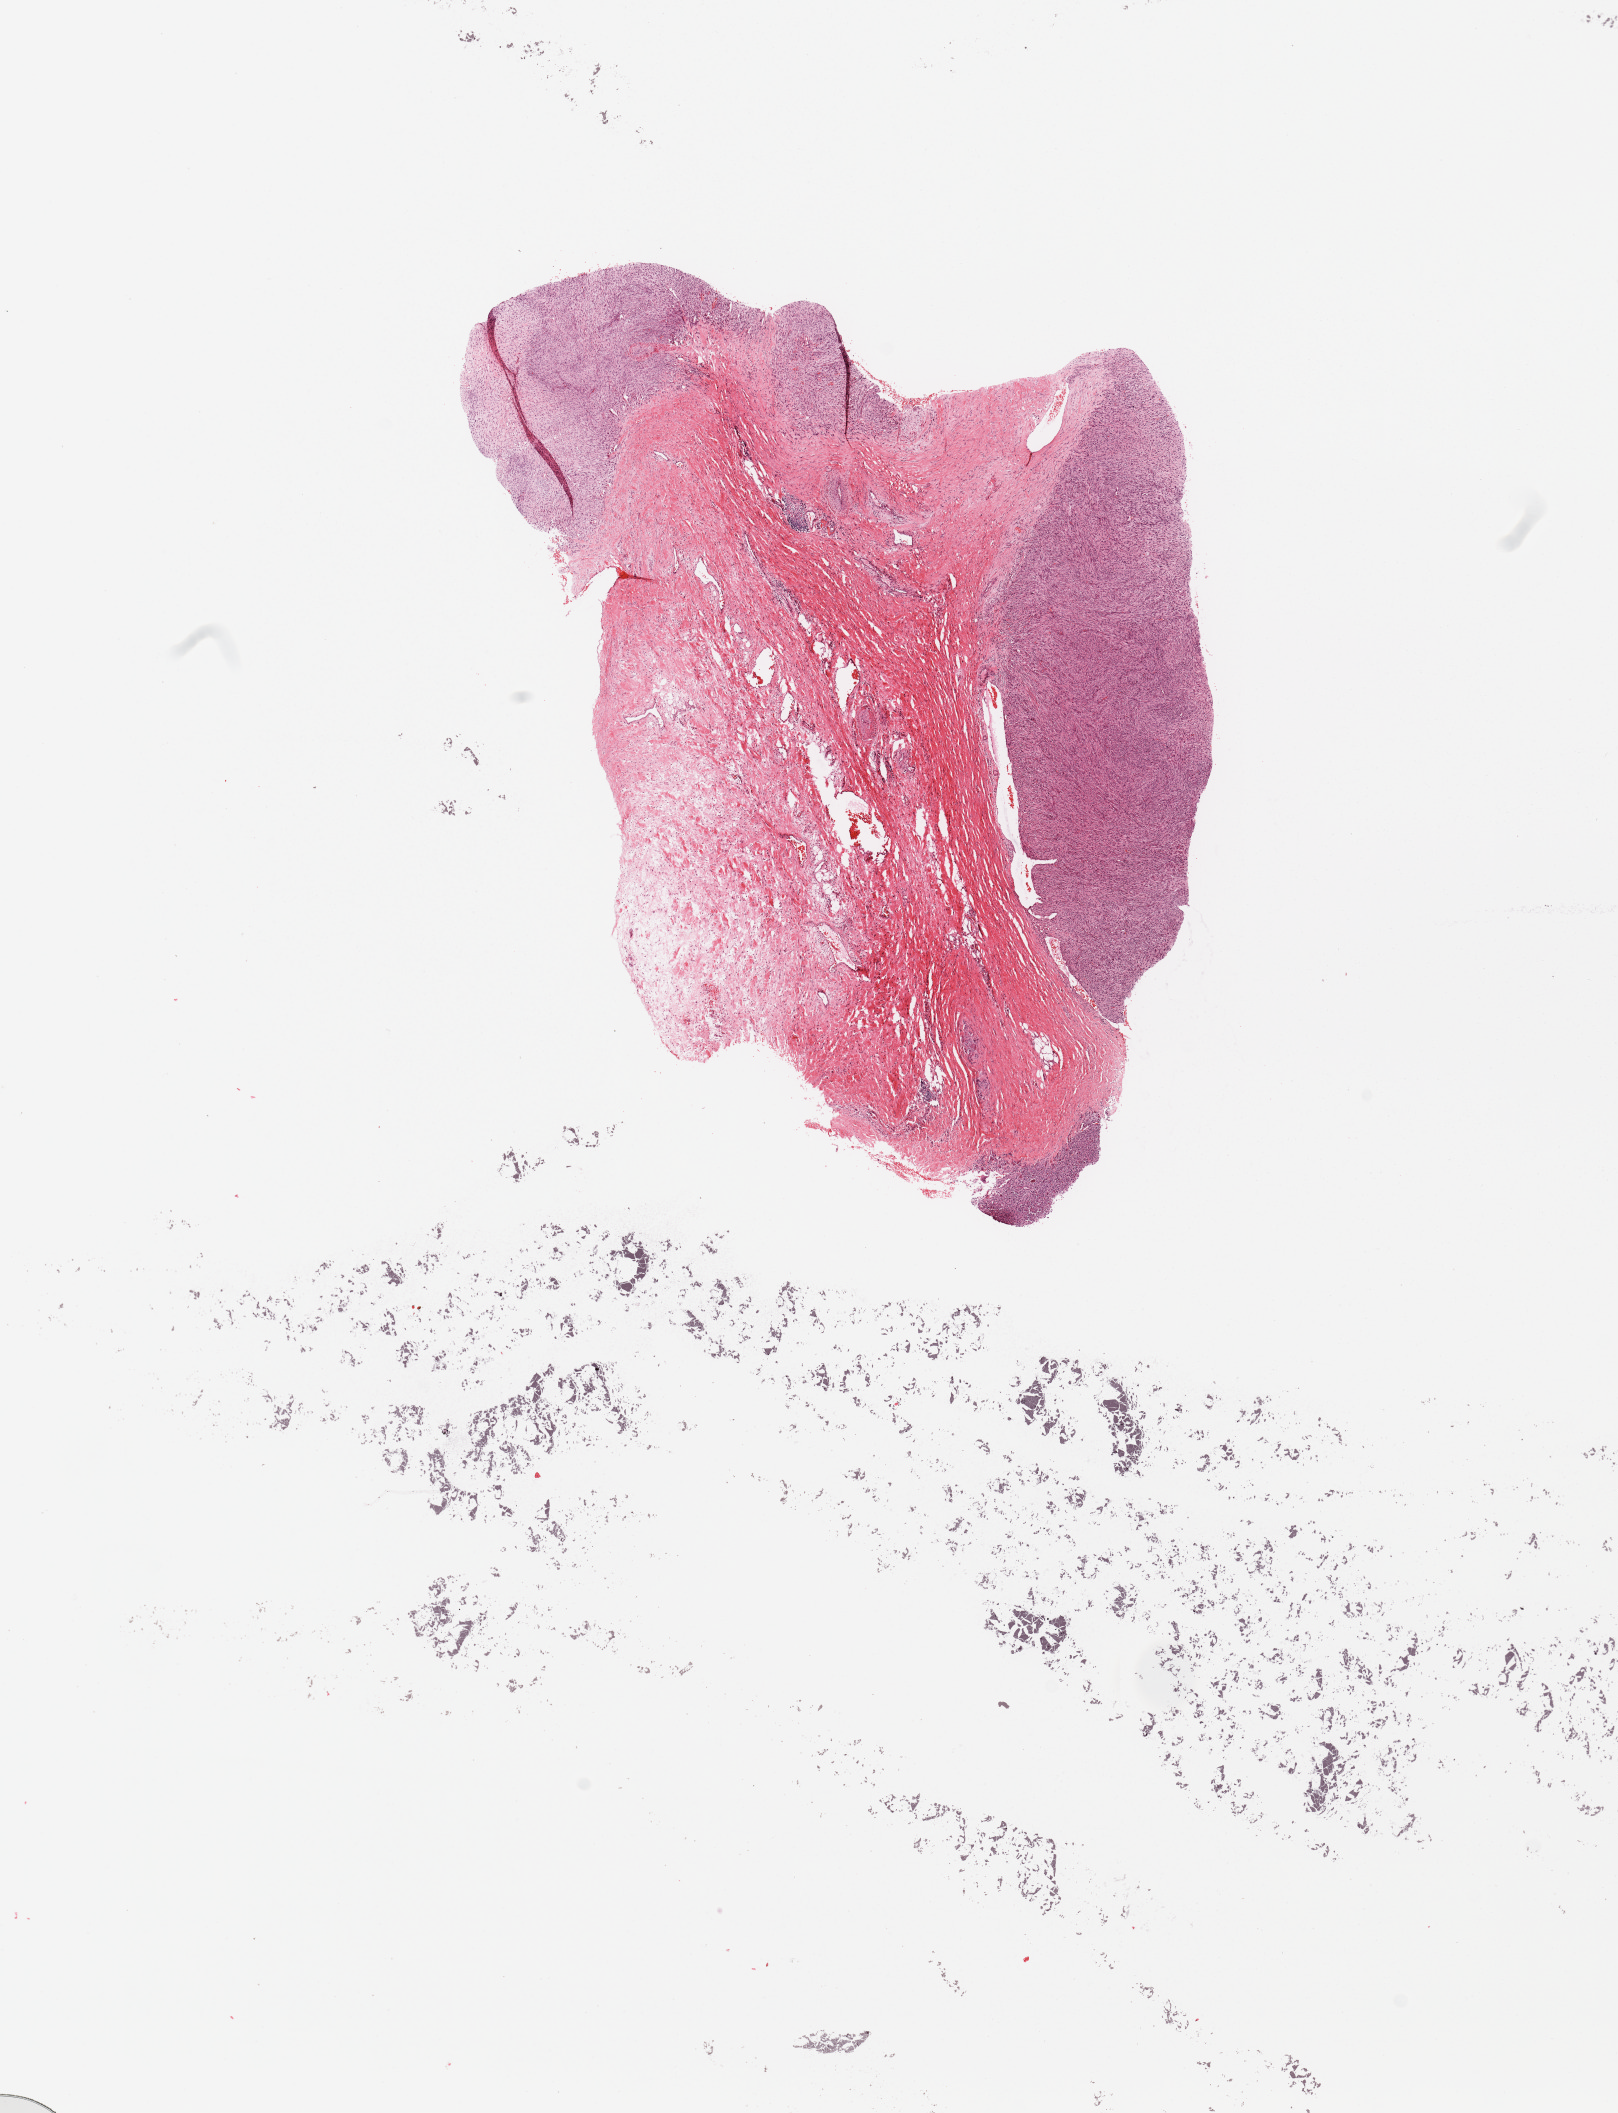
Digitized H&E-stained tissue section (whole slide), low-resolution overview of the scanned area, about 12.8 x 16.7 mm (from a 20x scan); tumour tissue sample. Male, 67 y/o.
Patient diagnosis (cohort enrolment): sarcoma (site not recorded at cohort level). Primary tumour site (as recorded): lower extremity.